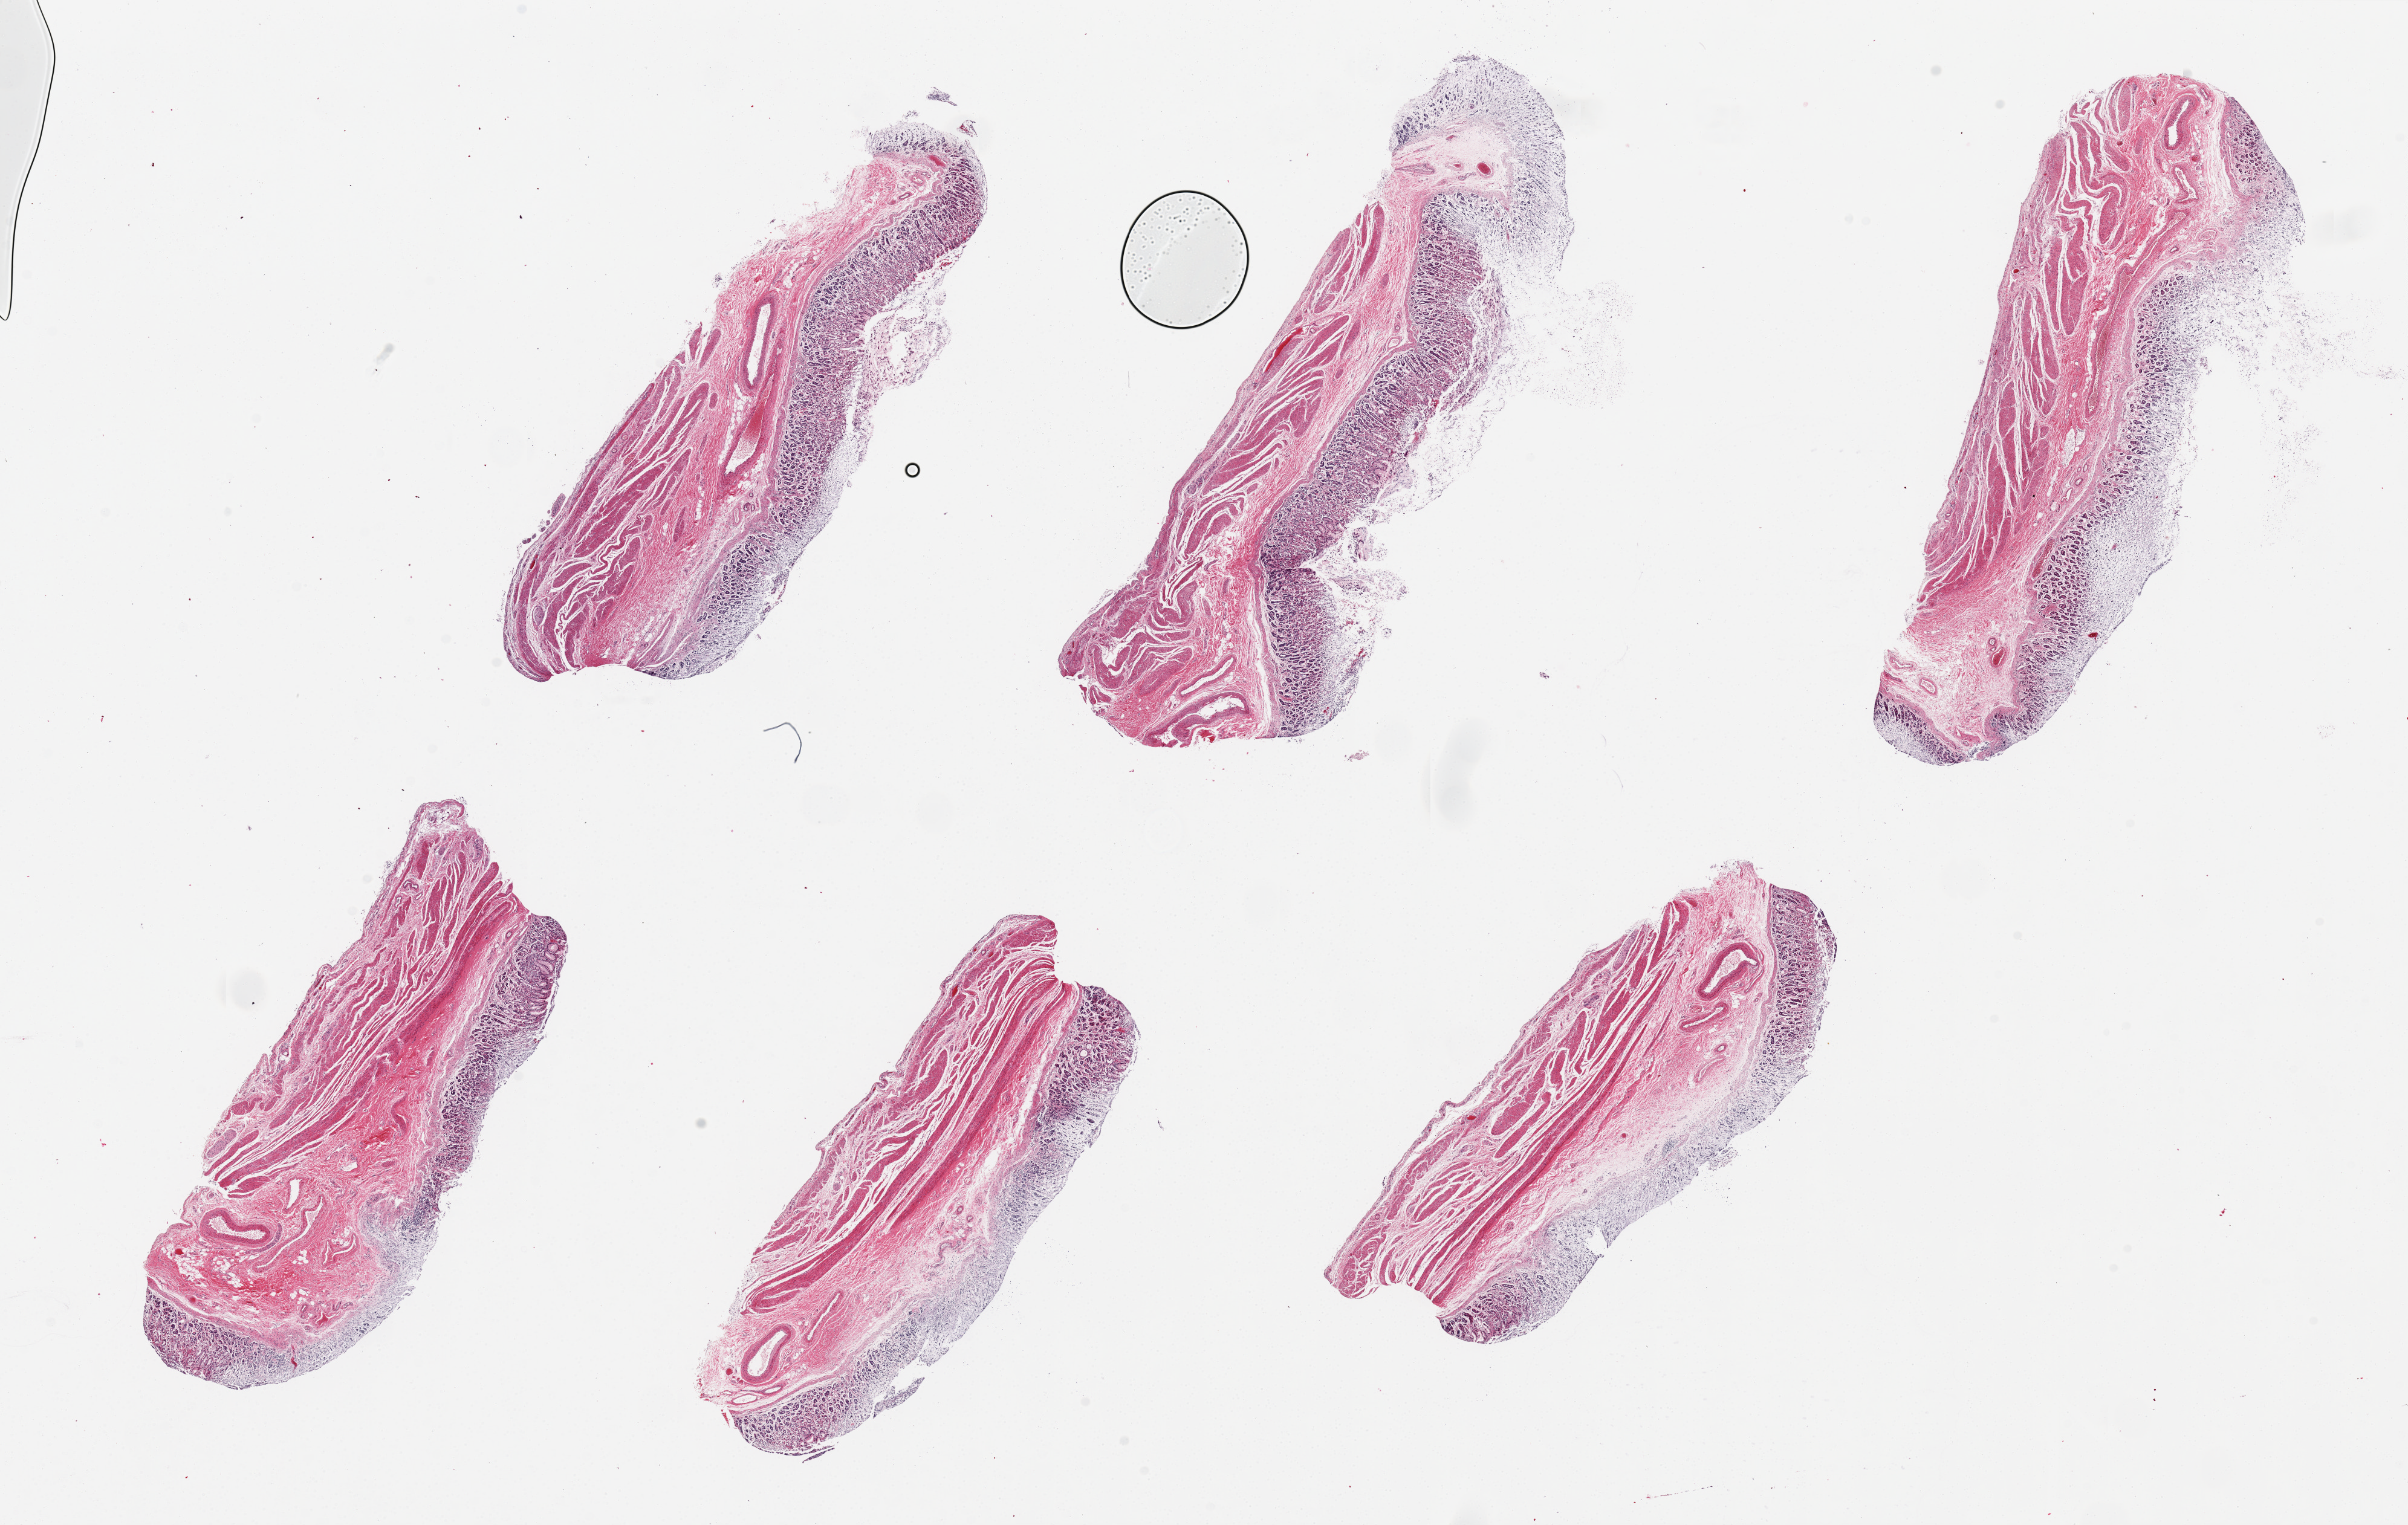
Whole-slide image, H&E stain, brightfield, shown as a low-resolution overview of the whole scanned area (about 31.5 x 20.0 mm, acquisition: 20x scan). PAXgene-fixed, paraffin-embedded tissue. Sampled site (target tissue): stomach. Donor tissue sample. Male donor.
- reviewer comment on this tissue sample: 6 pieces. Mucosa=3; muscle = 2